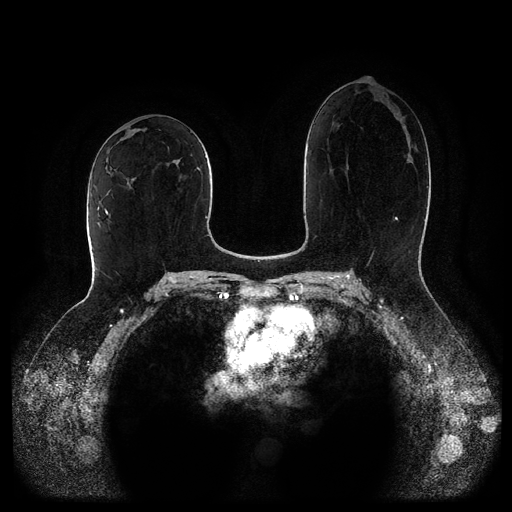
Breast MRI (dynamic contrast-enhanced, multi-phase), one axial slice. Position 51 of 116 along the scan axis. Dynamic contrast-enhanced series, time point 2 of 5 at this slice position (early post-contrast). 1.5 T. TE 2.6 ms, TR 5.2 ms. 512 × 512 image matrix. Female patient, age 52 years.
Outlined on this slice (semi-automatic segmentation, software-assisted and operator-edited):
- breast lesion (labelled 'tumour' in the annotation; benign lesions carry a separate 'benign' label): bounding box [x1, y1, x2, y2] px = [166, 158, 182, 167]